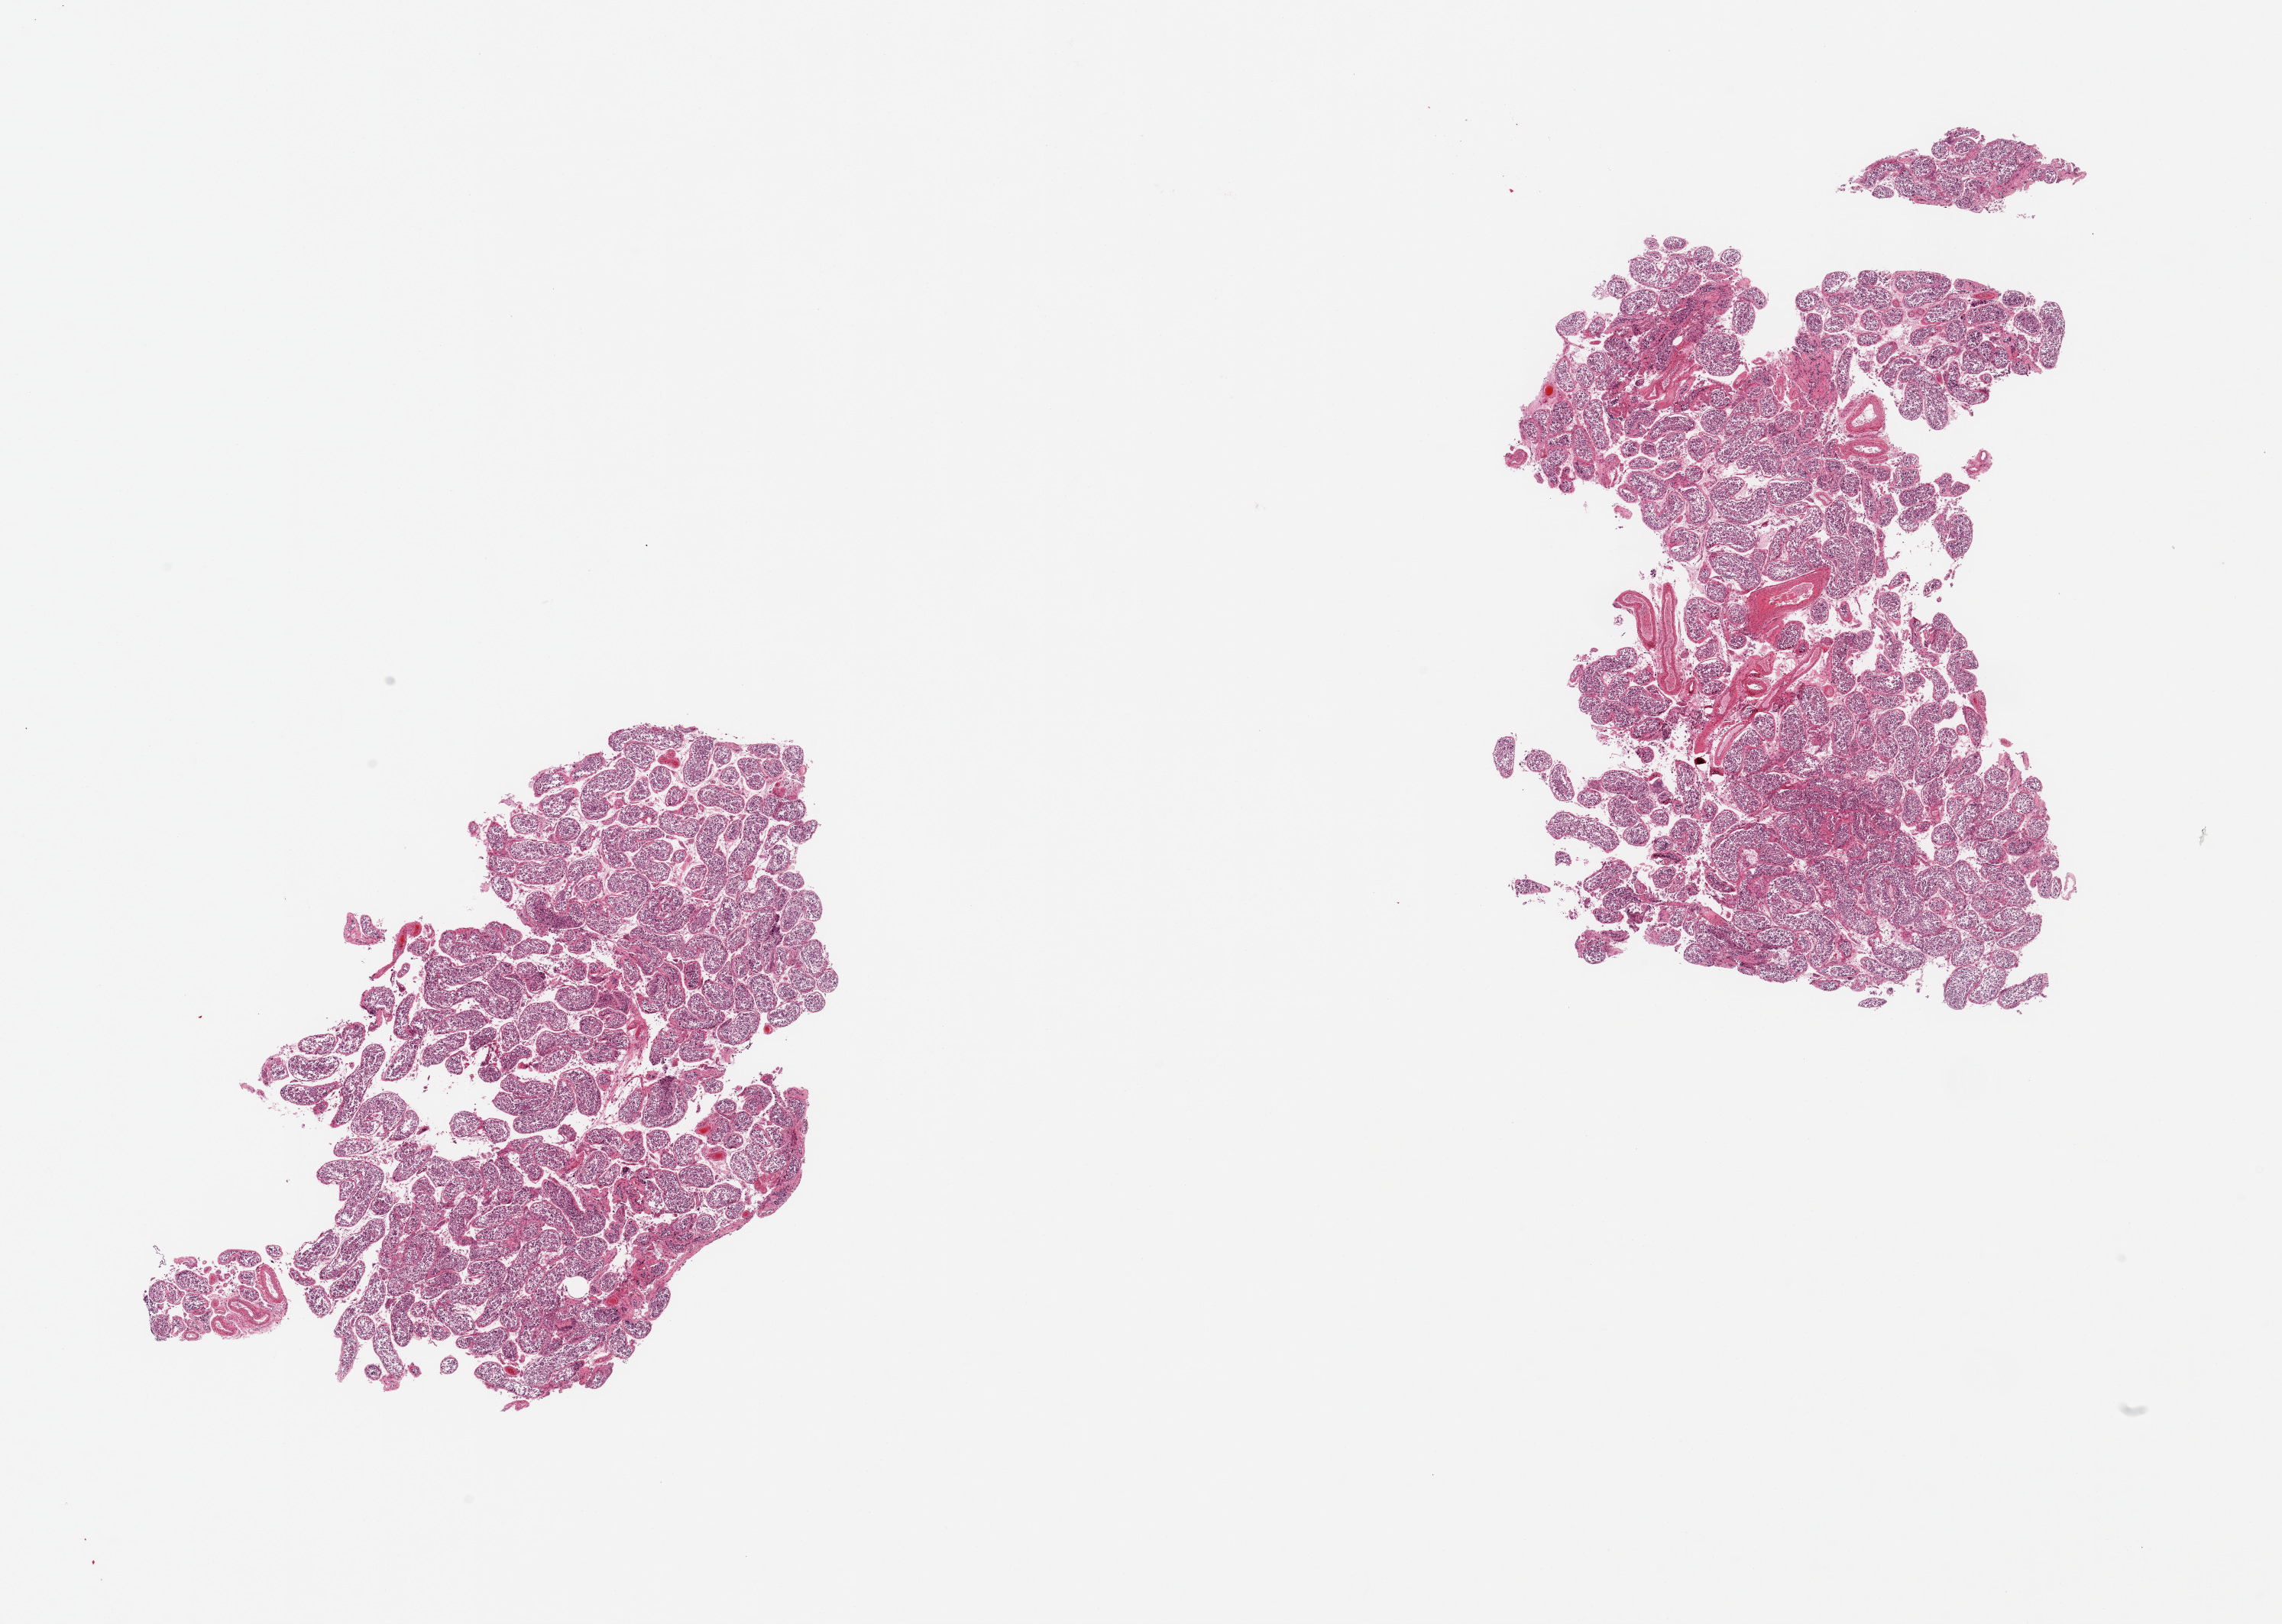
Digitized haematoxylin and eosin-stained section, brightfield — whole scanned area (about 23.6 x 16.8 mm) shown as a low-resolution overview. PAXgene-fixed, paraffin-embedded tissue. Target tissue: testis. Donor tissue sample. Donor sex: male.
Review note (as recorded): 2 pieces; spermatogenesis is present.